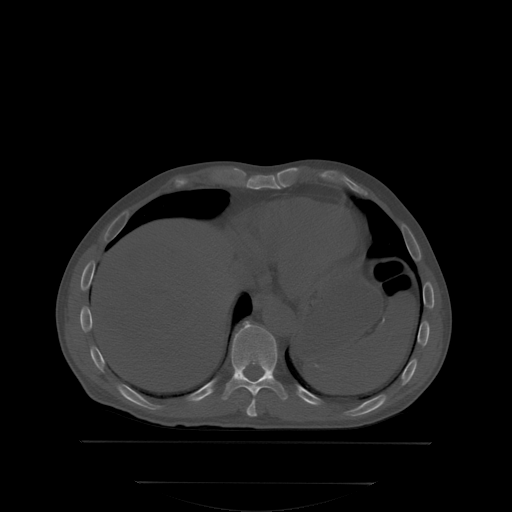
CT including the spine, one axial slice. Slice 194 of 350 in the series (ordered by position). Bone window (W 1800 / L 400 HU). 2.5 mm slice thickness. 512 × 512 image matrix. Male patient, age 58 years. From the clinical record (not read from this slice): primary cancer: prostate; vertebrae with lytic lesions (as recorded): L1.
Annotated regions visible in this slice (semi-automatic segmentation, software-assisted and operator-edited):
- T10 vertebra: box from (x=226, y=322) to (x=286, y=399) px
- T9 vertebra: (x=247, y=395)–(x=256, y=416)